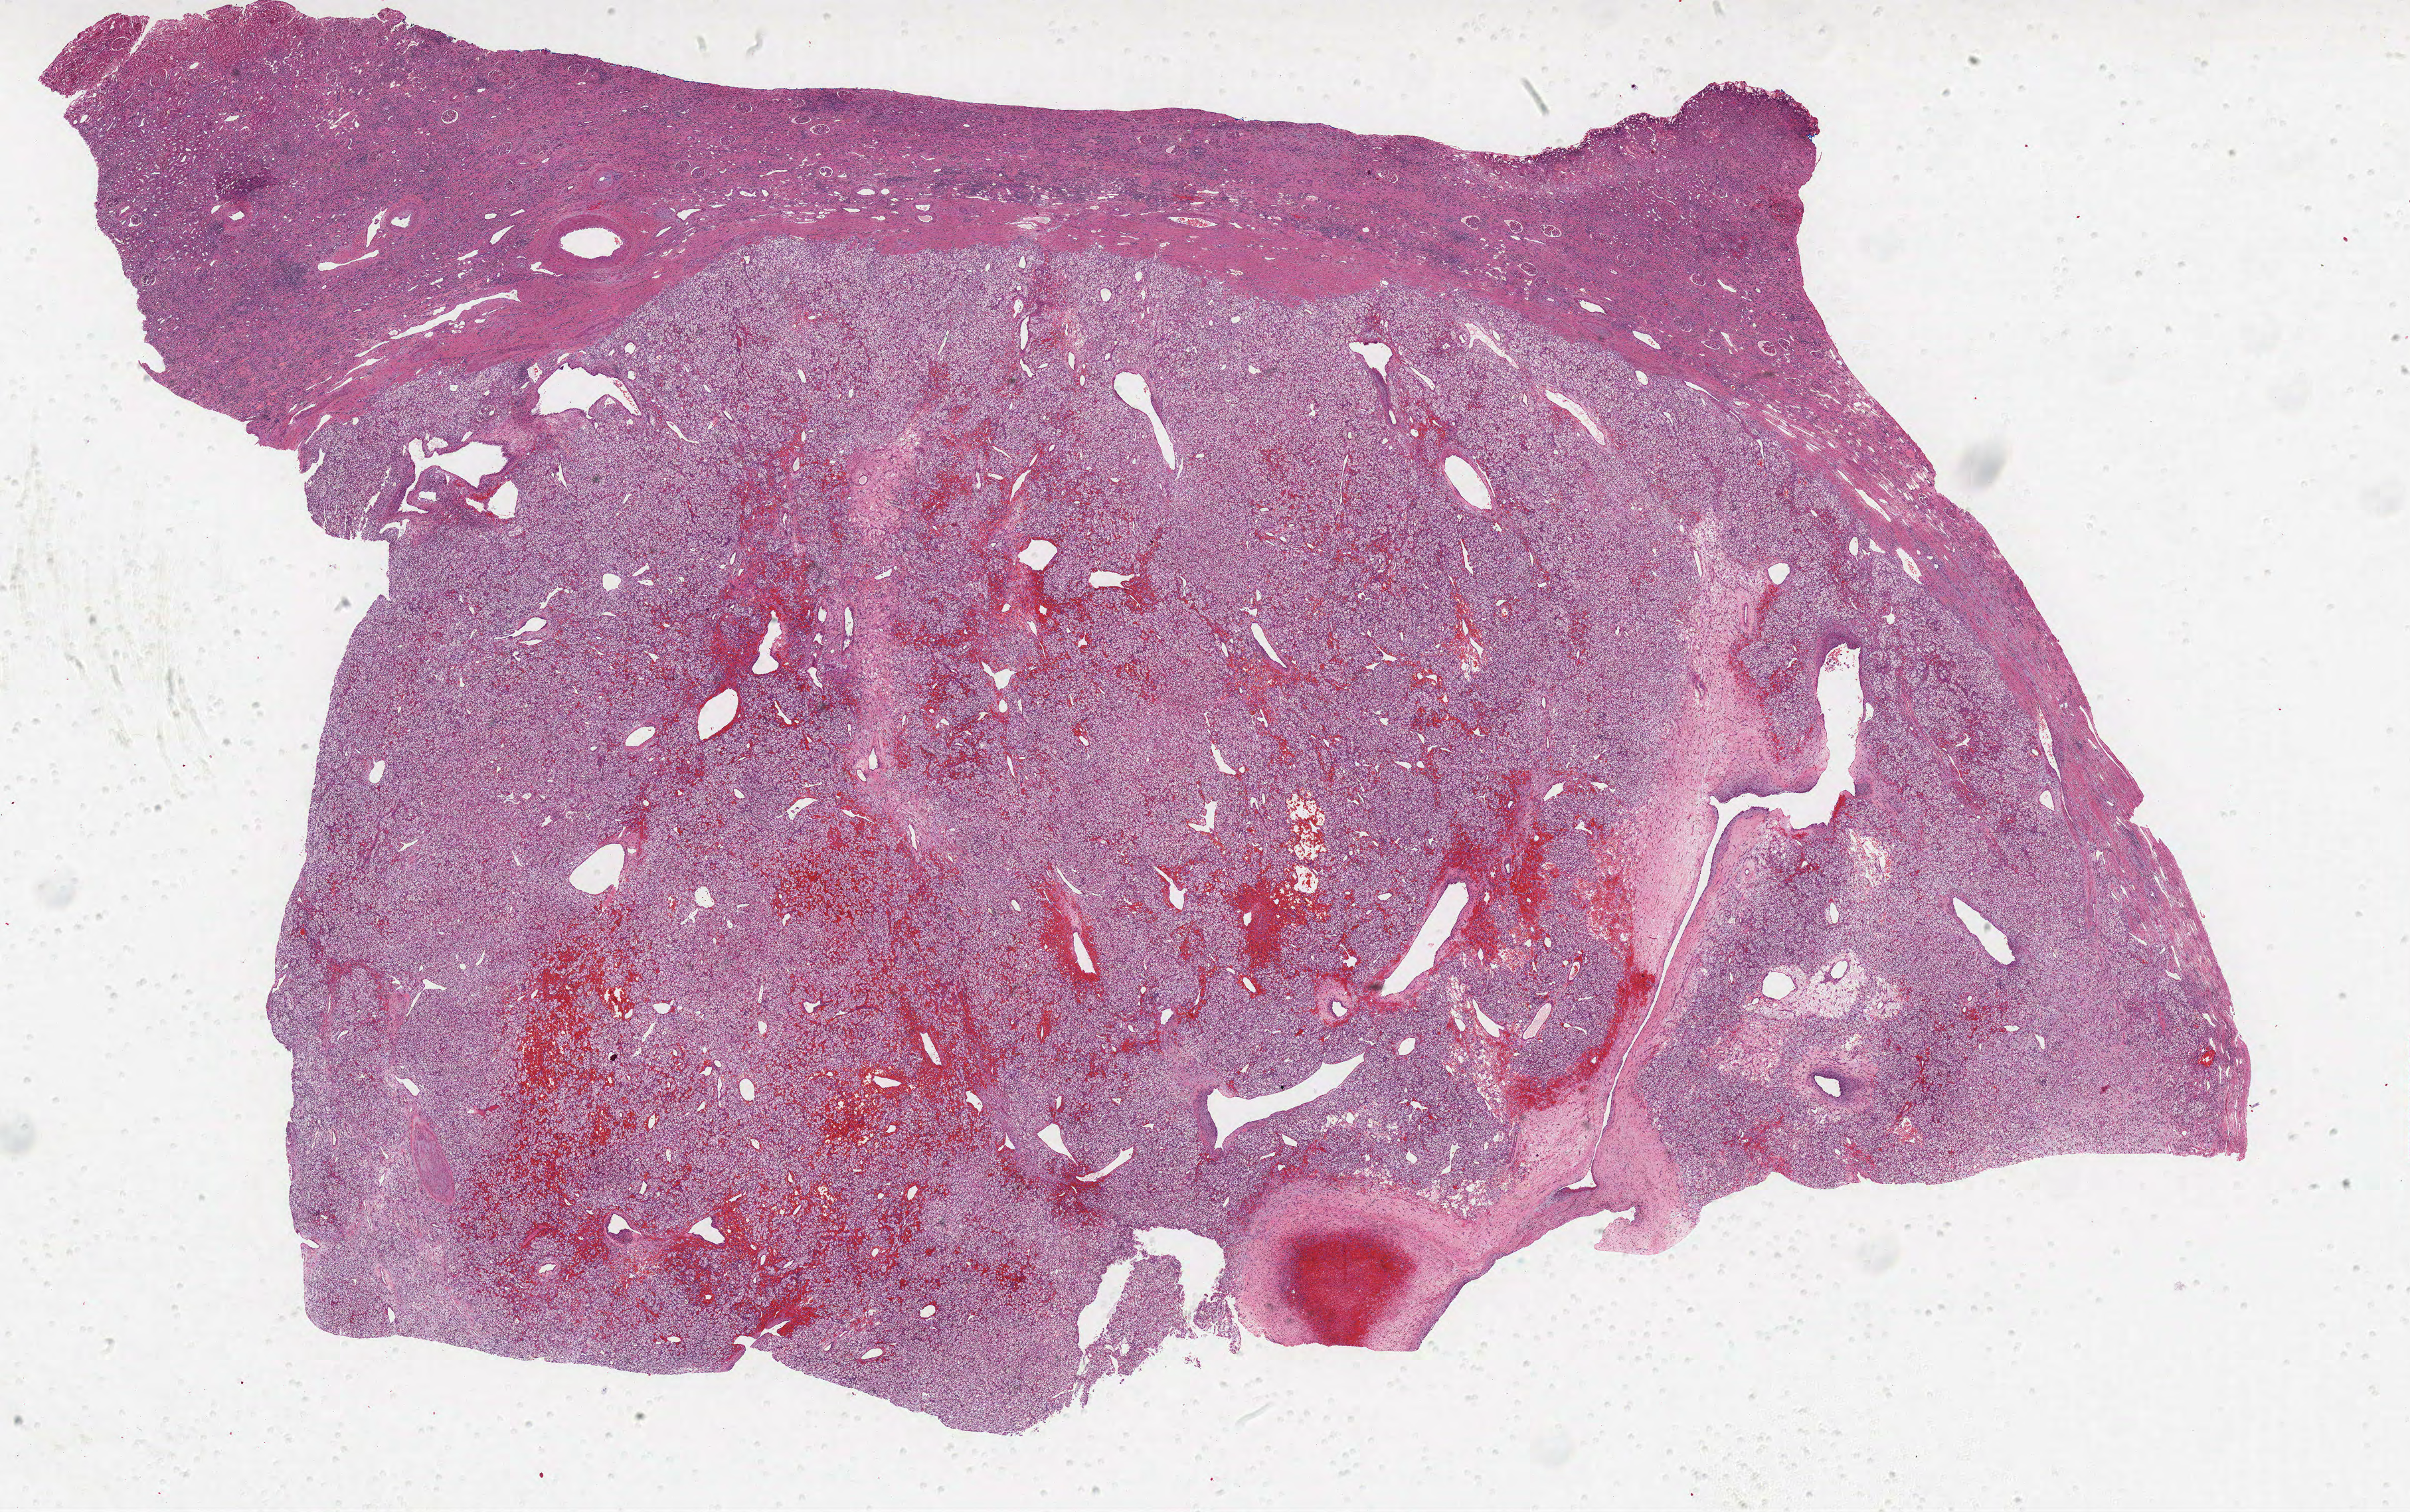
Whole-slide histology image, Hematoxylin and eosin (H&E) stained — whole scanned area (about 29.0 x 18.2 mm, slide scanned at 40x) shown as a low-resolution overview, FFPE section, sample: primary tumour, kidney. Male patient; age at initial diagnosis 42 years. Histologic grade: G3 (poorly differentiated).
Pathologic diagnosis: Clear cell adenocarcinoma, NOS. Laterality: left. AJCC pathologic stage: I.